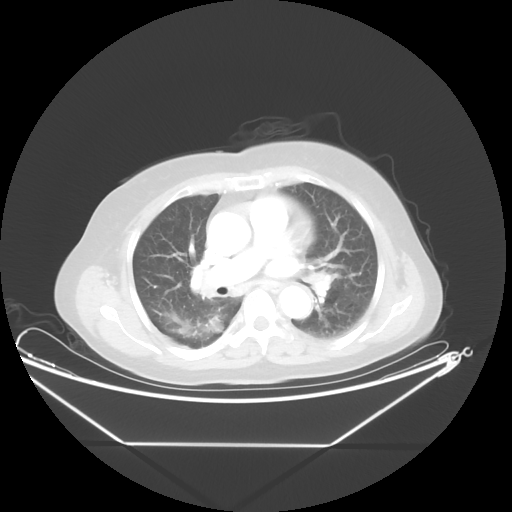
Chest CT, one axial slice; slice 26 of 48 in the series (ordered by position); reconstruction kernel STANDARD; 100 kVp; lung window (W 1500 / L -600 HU); 5 mm slice thickness; 512 × 512 image matrix, field of view 462 × 462 mm. Female patient, age 62 years. From the clinical record (not read from this slice): clinical TNM (as recorded): T1c N0 M0; histopathological grade: G2-3.
Annotated regions visible in this slice (bounding box drawn by a radiologist):
- lung tumour (recorded histology: adenocarcinoma): box from (x=203, y=306) to (x=237, y=346) px